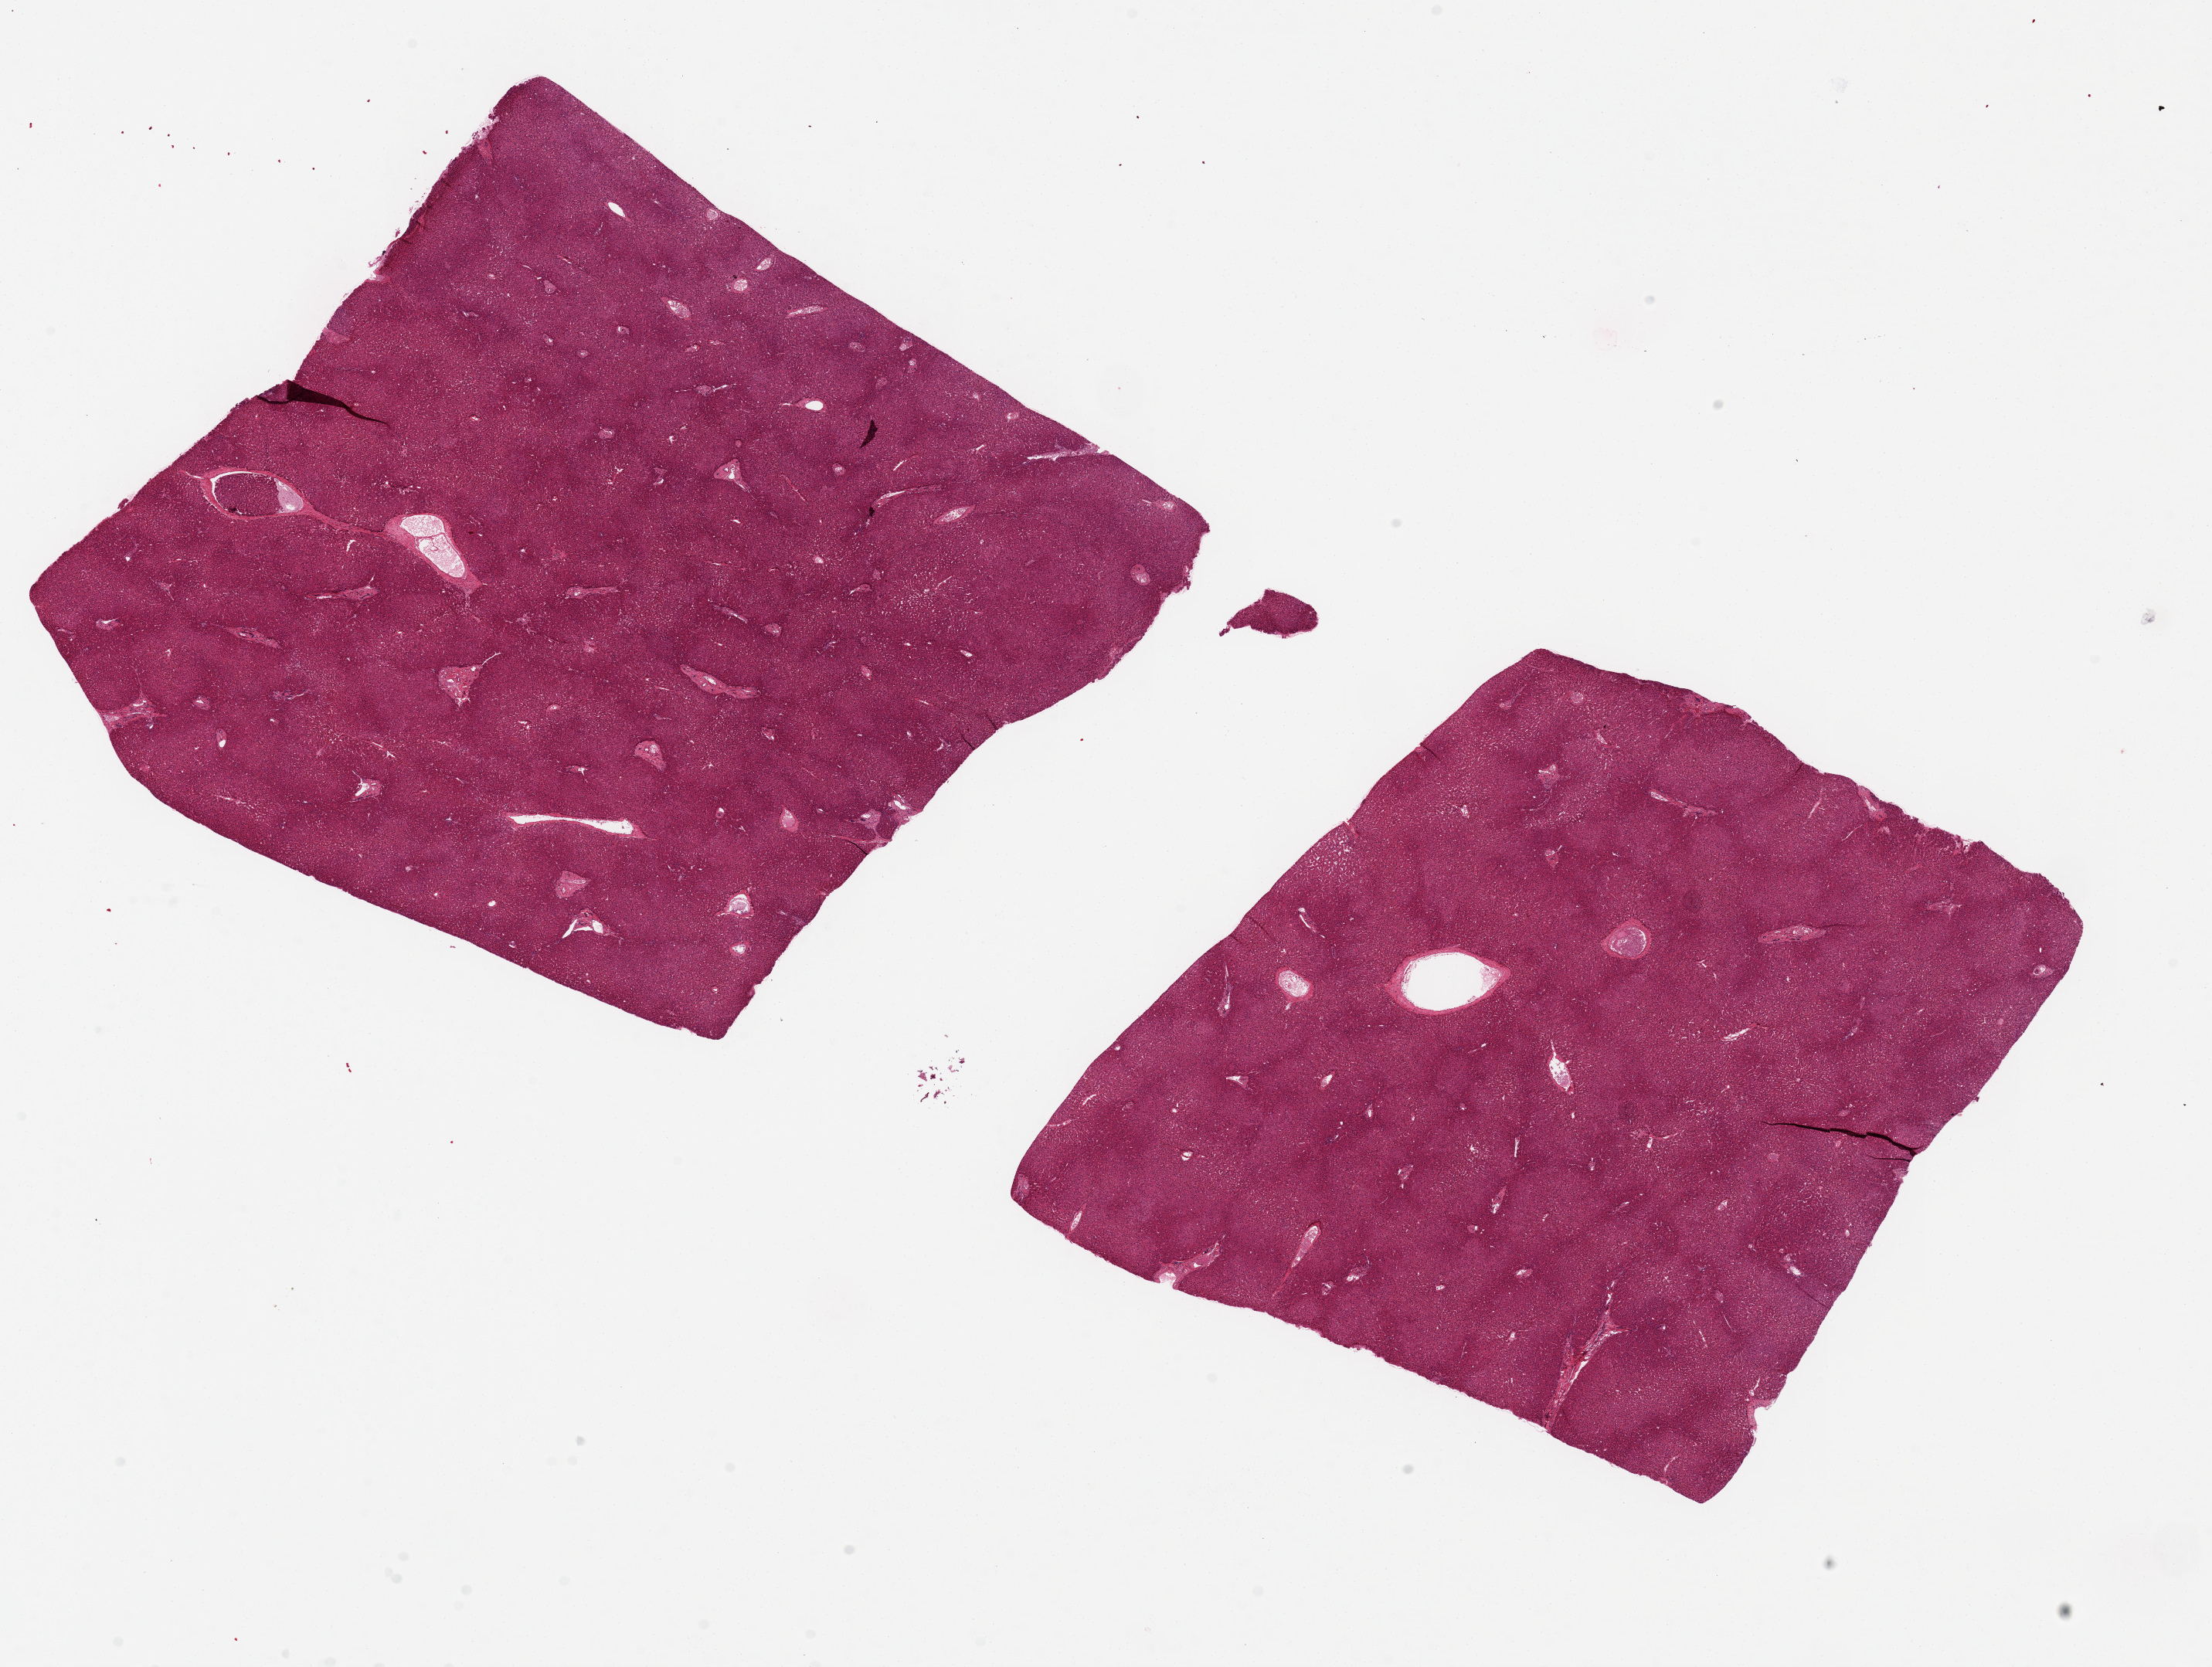
Whole-slide image, H&E stain, brightfield, whole scanned area (about 22.6 x 17.1 mm) shown as a low-resolution overview. PAXgene-fixed paraffin-embedded (PFPE) section. Target tissue: liver. Donor tissue sample. Donor sex: female.
• review note (as recorded): 2 aliquots, ~8x7mm. Moderate congestion